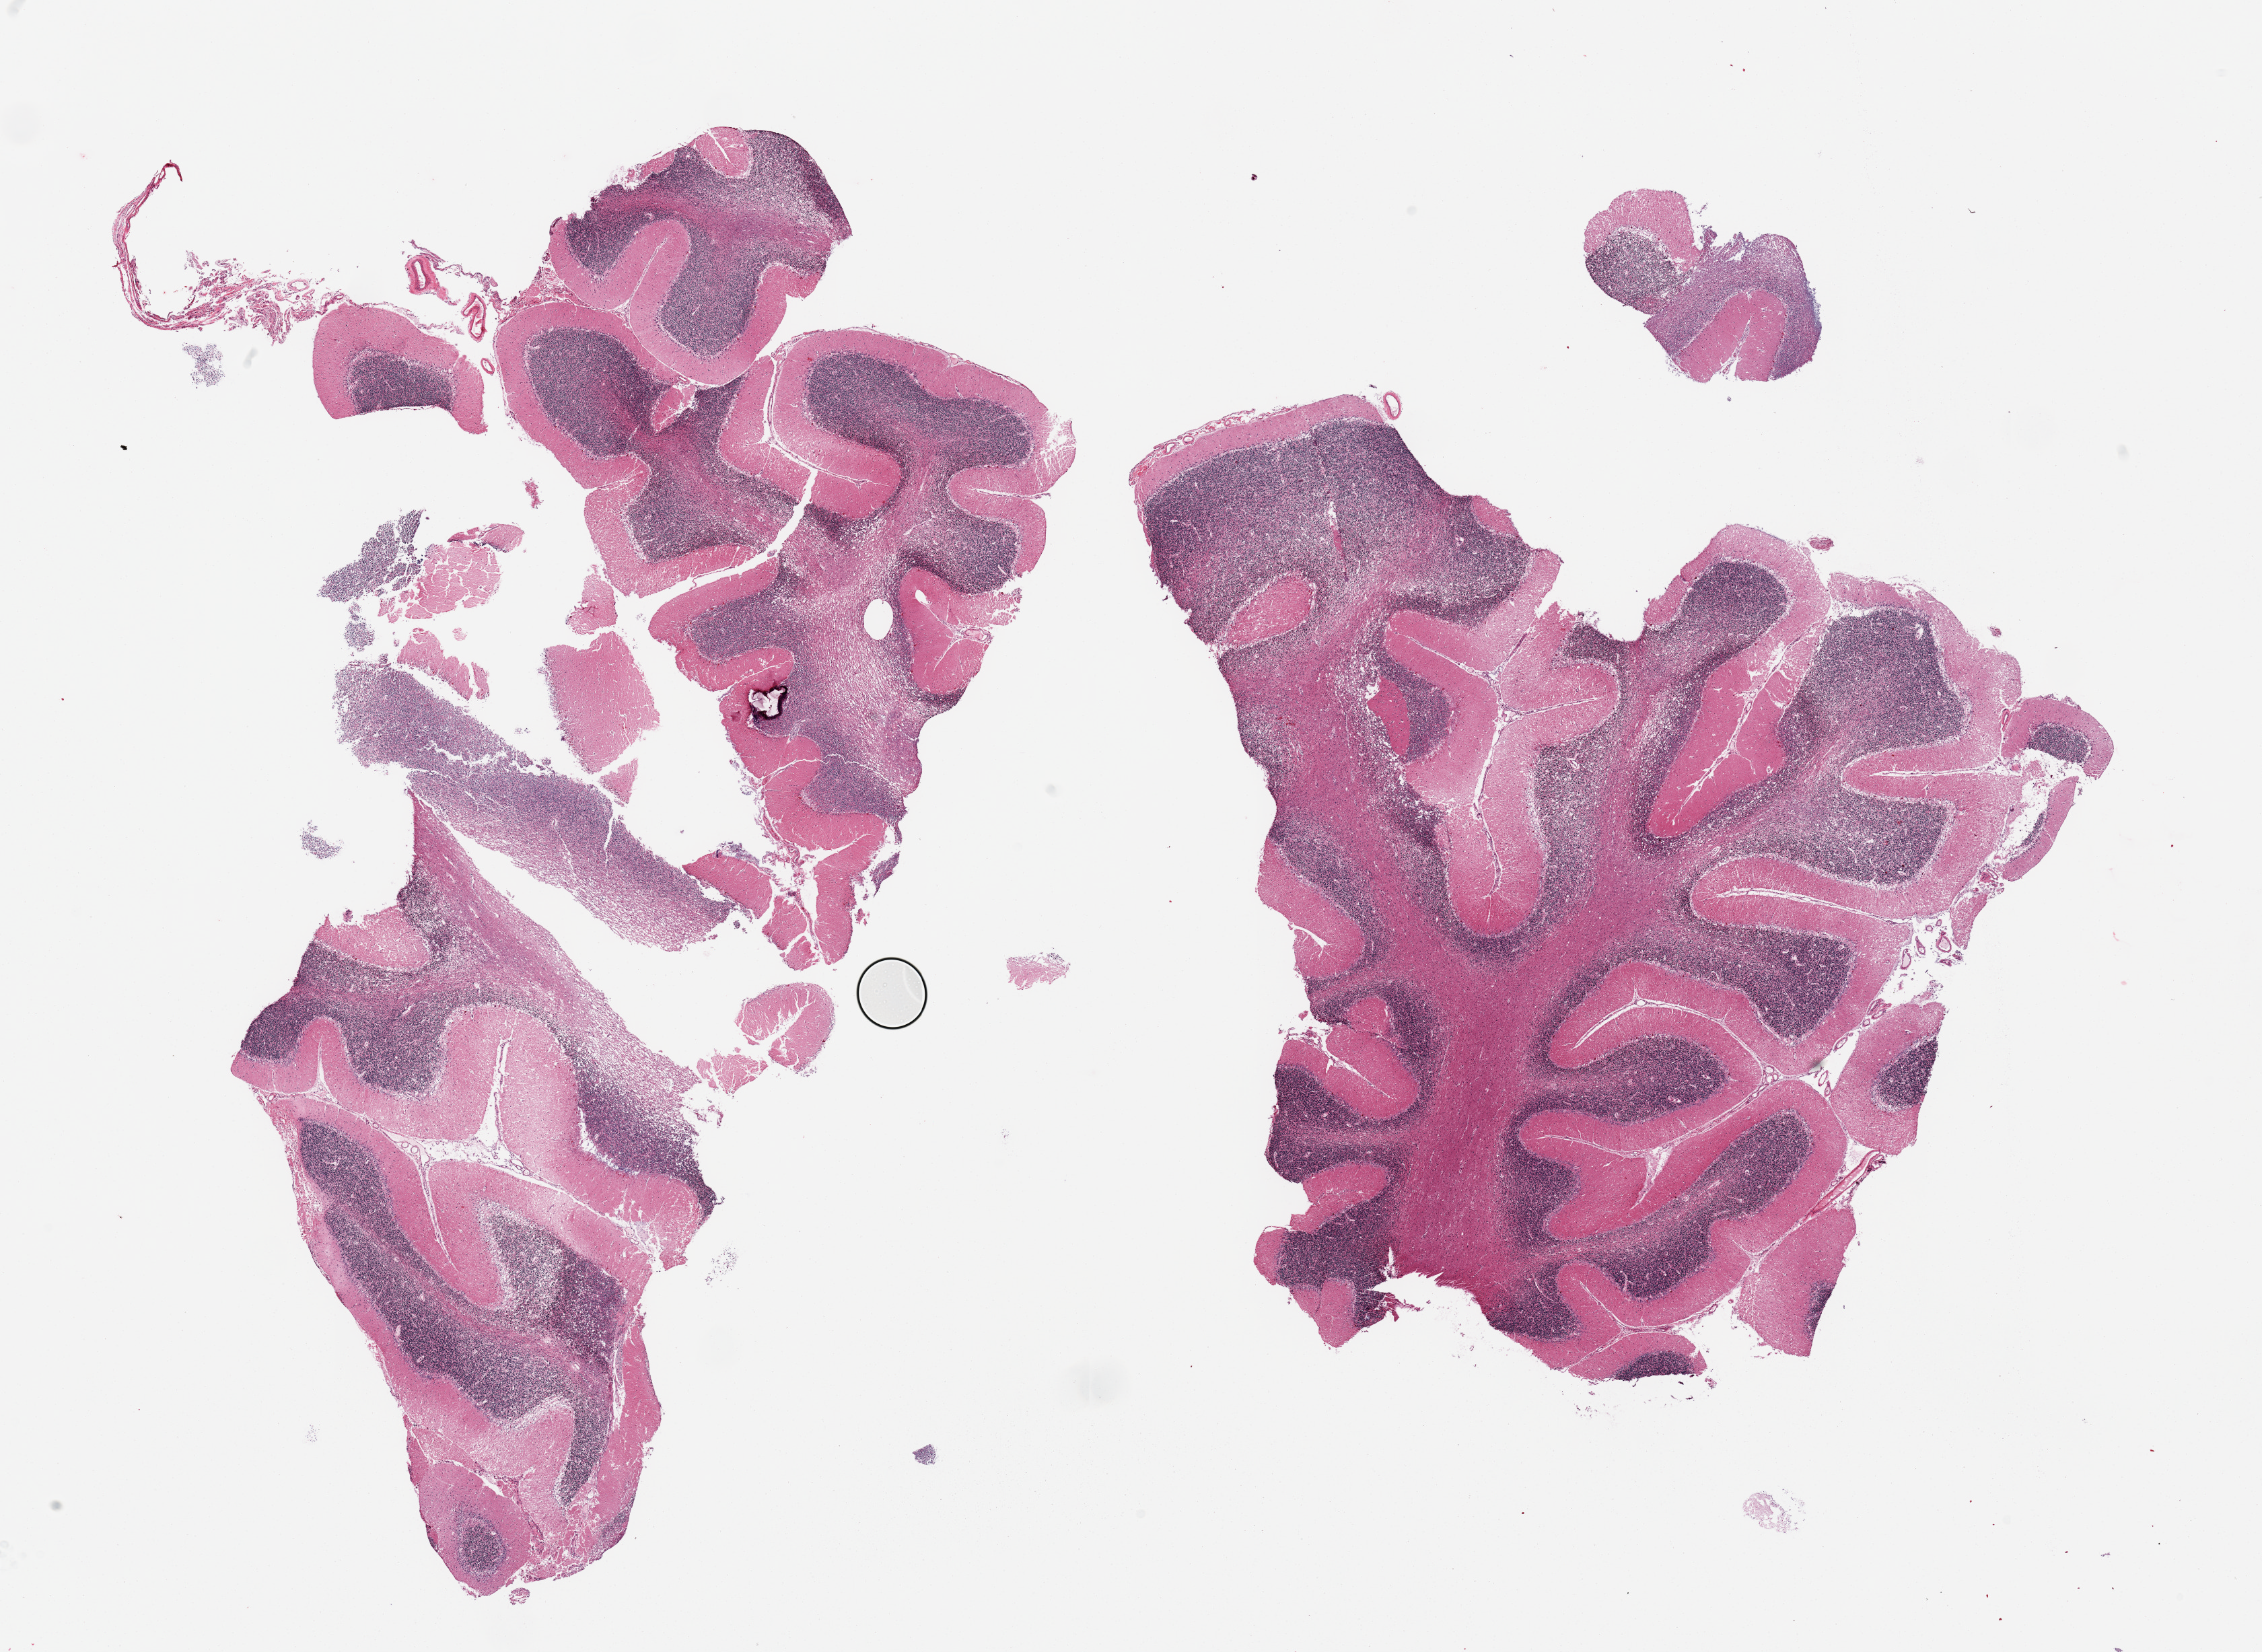
Digitized H&E-stained section — shown as a low-resolution overview of the whole scanned area (about 26.6 x 19.4 mm); PAXgene-fixed paraffin-embedded (PFPE) section; target tissue: cerebellum; tissue donor sample. Donor: male.
Pathologist's review note for this sample: 2 pieces, no abnormalities.